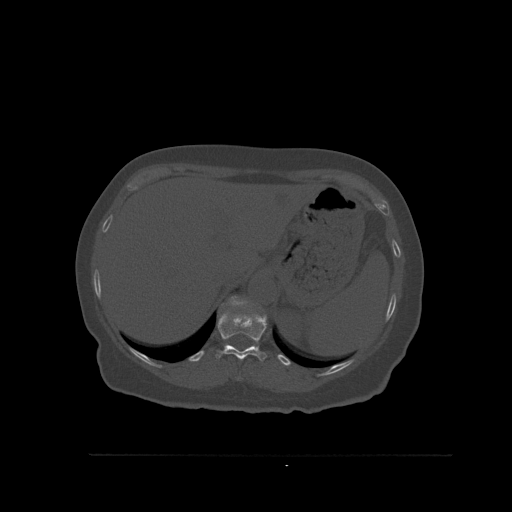
CT including the spine, one axial slice; position 302 of 527 along the scan axis; bone window (W 1800 / L 400 HU); 1.5 mm slice thickness; 512 × 512 image matrix, field of view 470 × 470 mm. Female patient, age 73 years. From the clinical record (not read from this slice): primary cancer: breast.
Annotated regions visible in this slice (semi-automatically segmented with operator editing):
- T11 vertebra: bounding box [x1, y1, x2, y2] px = [215, 311, 267, 362]
- T12 vertebra: [222, 296, 255, 310]